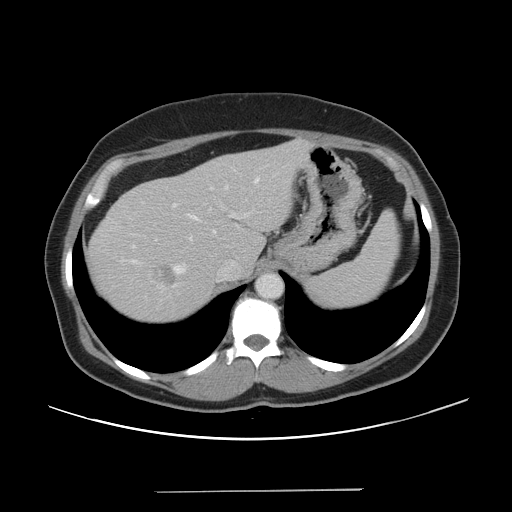
Contrast-enhanced abdominal CT, one axial slice; position 35 of 56 along the scan axis; 120 kVp; intravenous contrast given; soft-tissue window (W 400 / L 40 HU); 5 mm slice thickness; 512 × 512 image matrix, field of view 419 × 419 mm. Female patient, age 54 years. Case-level facts recorded for this patient, not image findings: diagnosis: colorectal cancer liver metastases, imaged before liver resection; multiple liver metastases: yes; largest metastasis: 3.2 cm.
Annotated regions visible in this slice (manually delineated by an expert):
- hepatic veins: bounding box (x1, y1, x2, y2) in pixels: (120, 177, 260, 275)
- liver: (88, 140, 311, 325)
- planned liver remnant (the part of the liver to remain after resection): (187, 140, 311, 272)
- portal vein (with intrahepatic branches): (208, 184, 241, 219)
- liver metastasis: (154, 265, 176, 287)